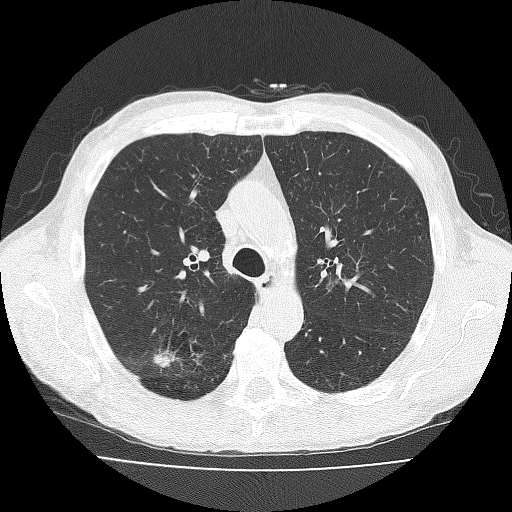
Low-dose screening chest CT, axial slice; third annual screen; lung window (W 1500 / L -600 HU); 120 kVp; 512 × 512 image matrix. Male, age 73 years at enrolment. Current smoker at enrolment.
Expert reader's lesion annotation, bounding box [x1, y1, x2, y2] px = [140, 332, 190, 379]. The exam's reader record, not a measurement of the box and not confirmed to be the same lesion: non-calcified nodule or mass ≥4 mm, right upper lobe, 11 × 10 mm, spiculated (stellate) margins, soft tissue attenuation, pre-existing on the prior screen: no. Official screen result: positive, other. Participant outcome: lung cancer diagnosed 38 days after this screen — adenosquamous carcinoma, right upper lobe, well differentiated (G1), stage IA (AJCC 6th edition), 20 mm at pathology.